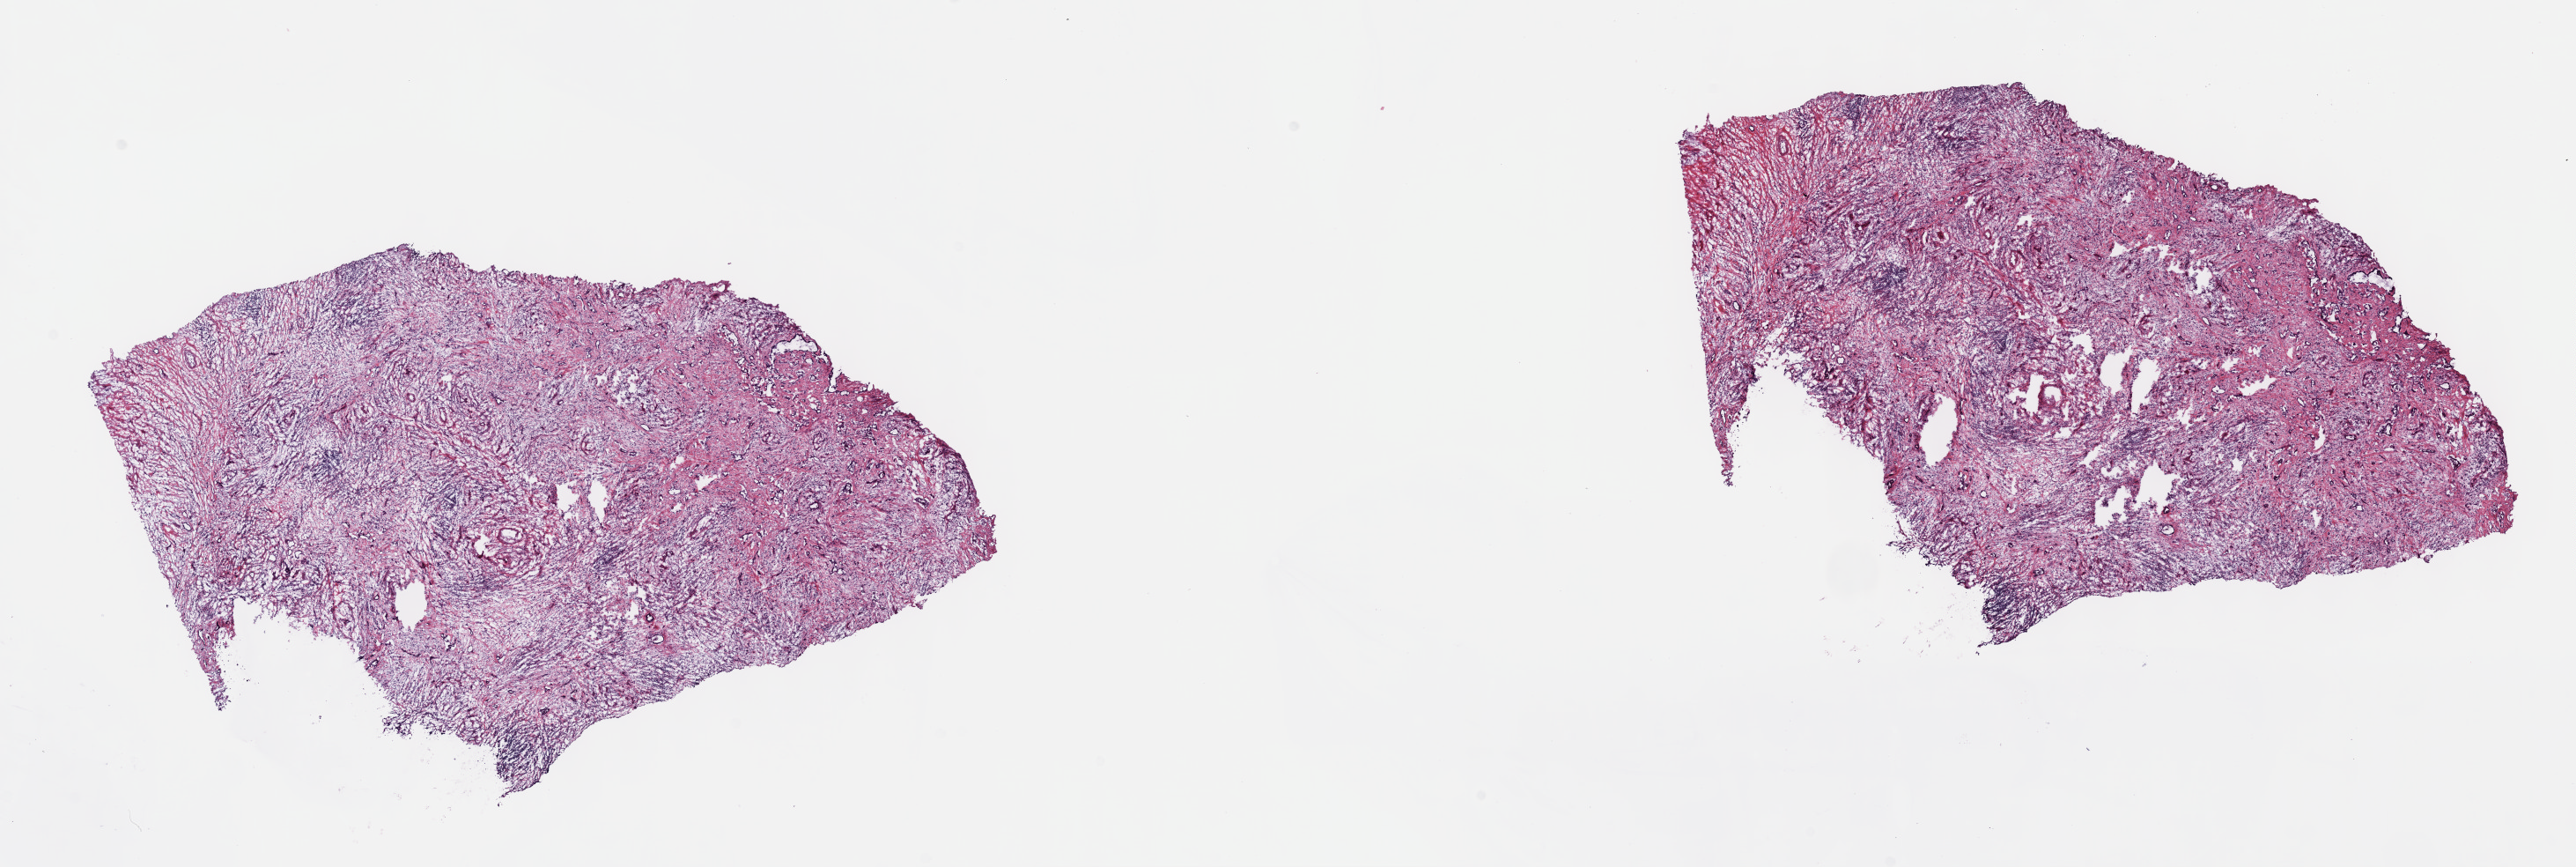
Whole-slide histology image, Hematoxylin and eosin (H&E) stained — whole scanned area (about 23.7 x 8.0 mm, acquisition: 40x scan) shown as a low-resolution overview; frozen section from the top of the tissue portion; bile duct, primary tumour sample. Male, age 72 years at initial diagnosis. Histologic grade: G2 (moderately differentiated). Slide review estimates, as recorded: tumour cells 60%, tumour nuclei 60%, normal cells 0%, stromal cells 40%, necrosis 0%. Infiltration values recorded for this section: lymphocyte infiltration 9%, monocyte infiltration 2%, neutrophil infiltration 5%.
Histologic diagnosis: Cholangiocarcinoma (intrahepatic bile duct). AJCC pathologic stage: I (7th edition).